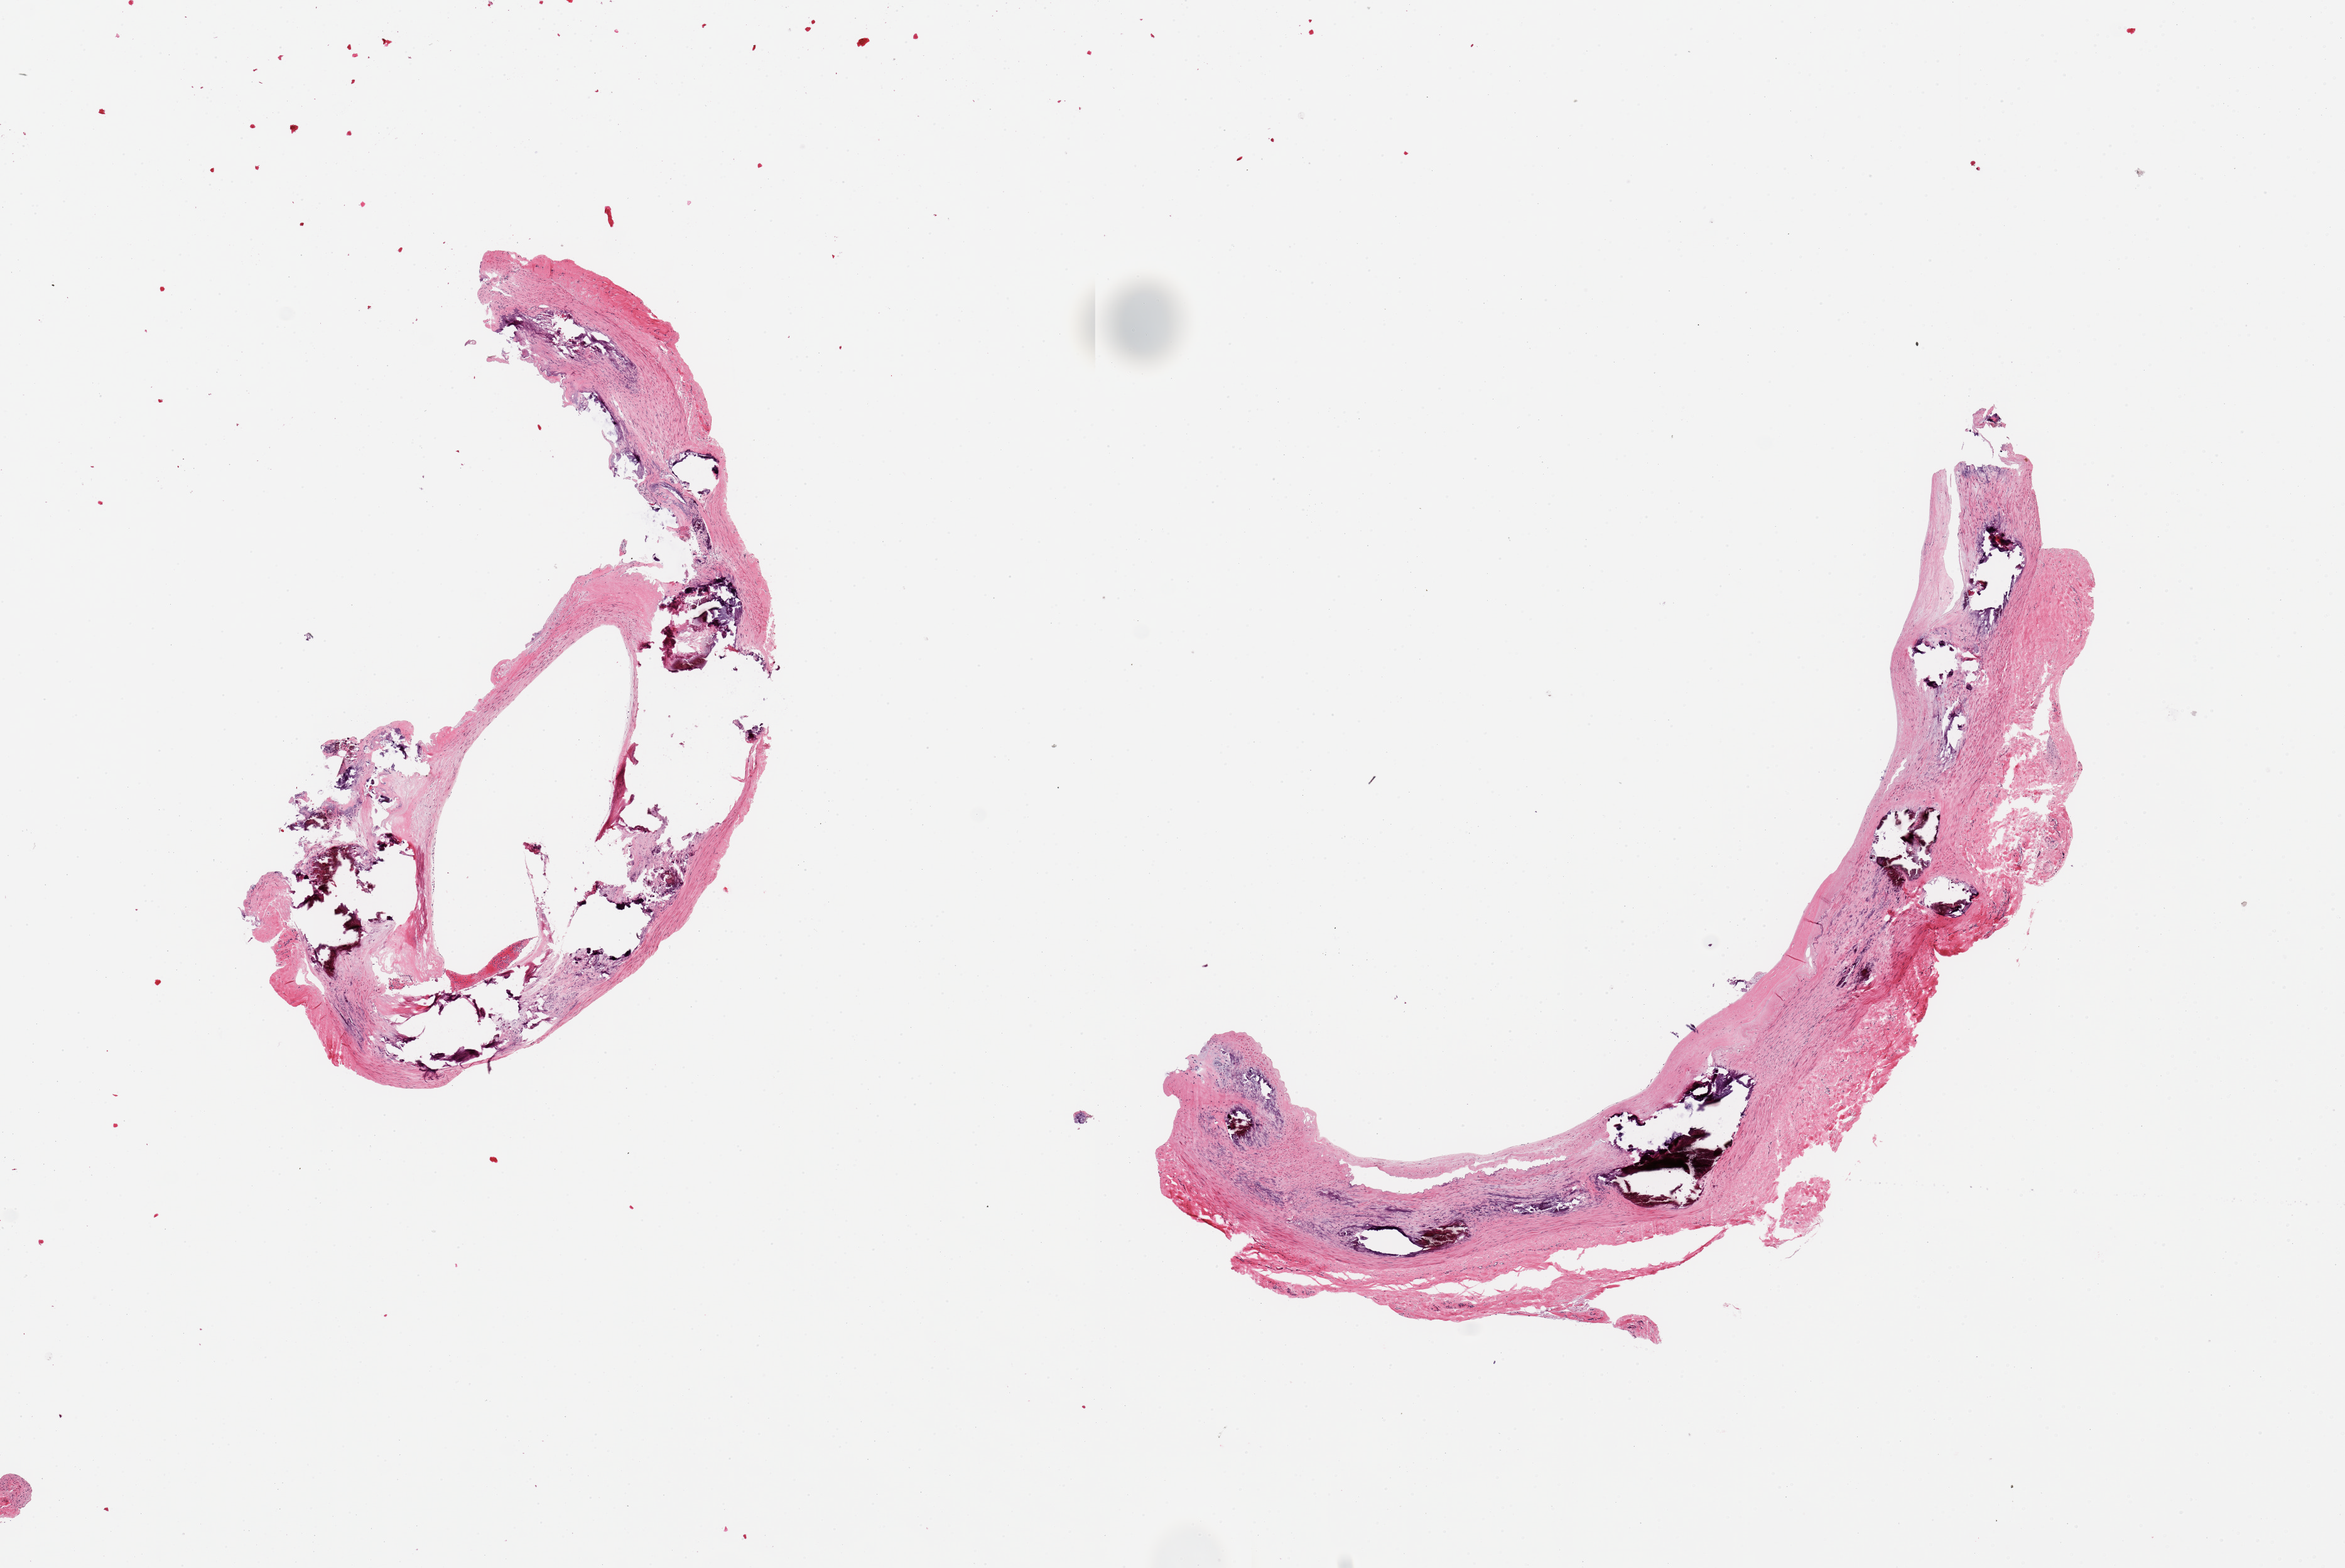
Hematoxylin and eosin (H&E) whole-slide image — a low-resolution overview of the entire scanned area, about 14.8 x 9.9 mm (acquisition: 20x scan); PAXgene-fixed paraffin-embedded (PFPE) section; section of tibial artery (target tissue); donor tissue sample.
• review note (as recorded): 2 pieces(fragemented), partially occlusive calcifying atherosis